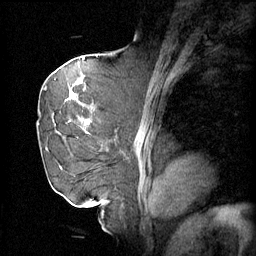
Breast MRI (dynamic contrast-enhanced), one sagittal slice. Position 34 of 60 along the scan axis. 4 images stored at this slice position (order not interpretable as contrast timing). 1.5 T. TE 4.2 ms, TR 11 ms. 256 × 256 image matrix, field of view 220 × 220 mm. Female patient, age 72 years.
Annotated regions visible in this slice (semi-automatically segmented with operator editing):
- analysis volume of interest (the breast-tissue region the enhancement analysis was run in; not a lesion): bounding box [x1, y1, x2, y2] px = [44, 68, 109, 161]
- tumour enhancement mask (voxels above the 70 % enhancement threshold inside the analysis volume of interest): [52, 76, 100, 133]